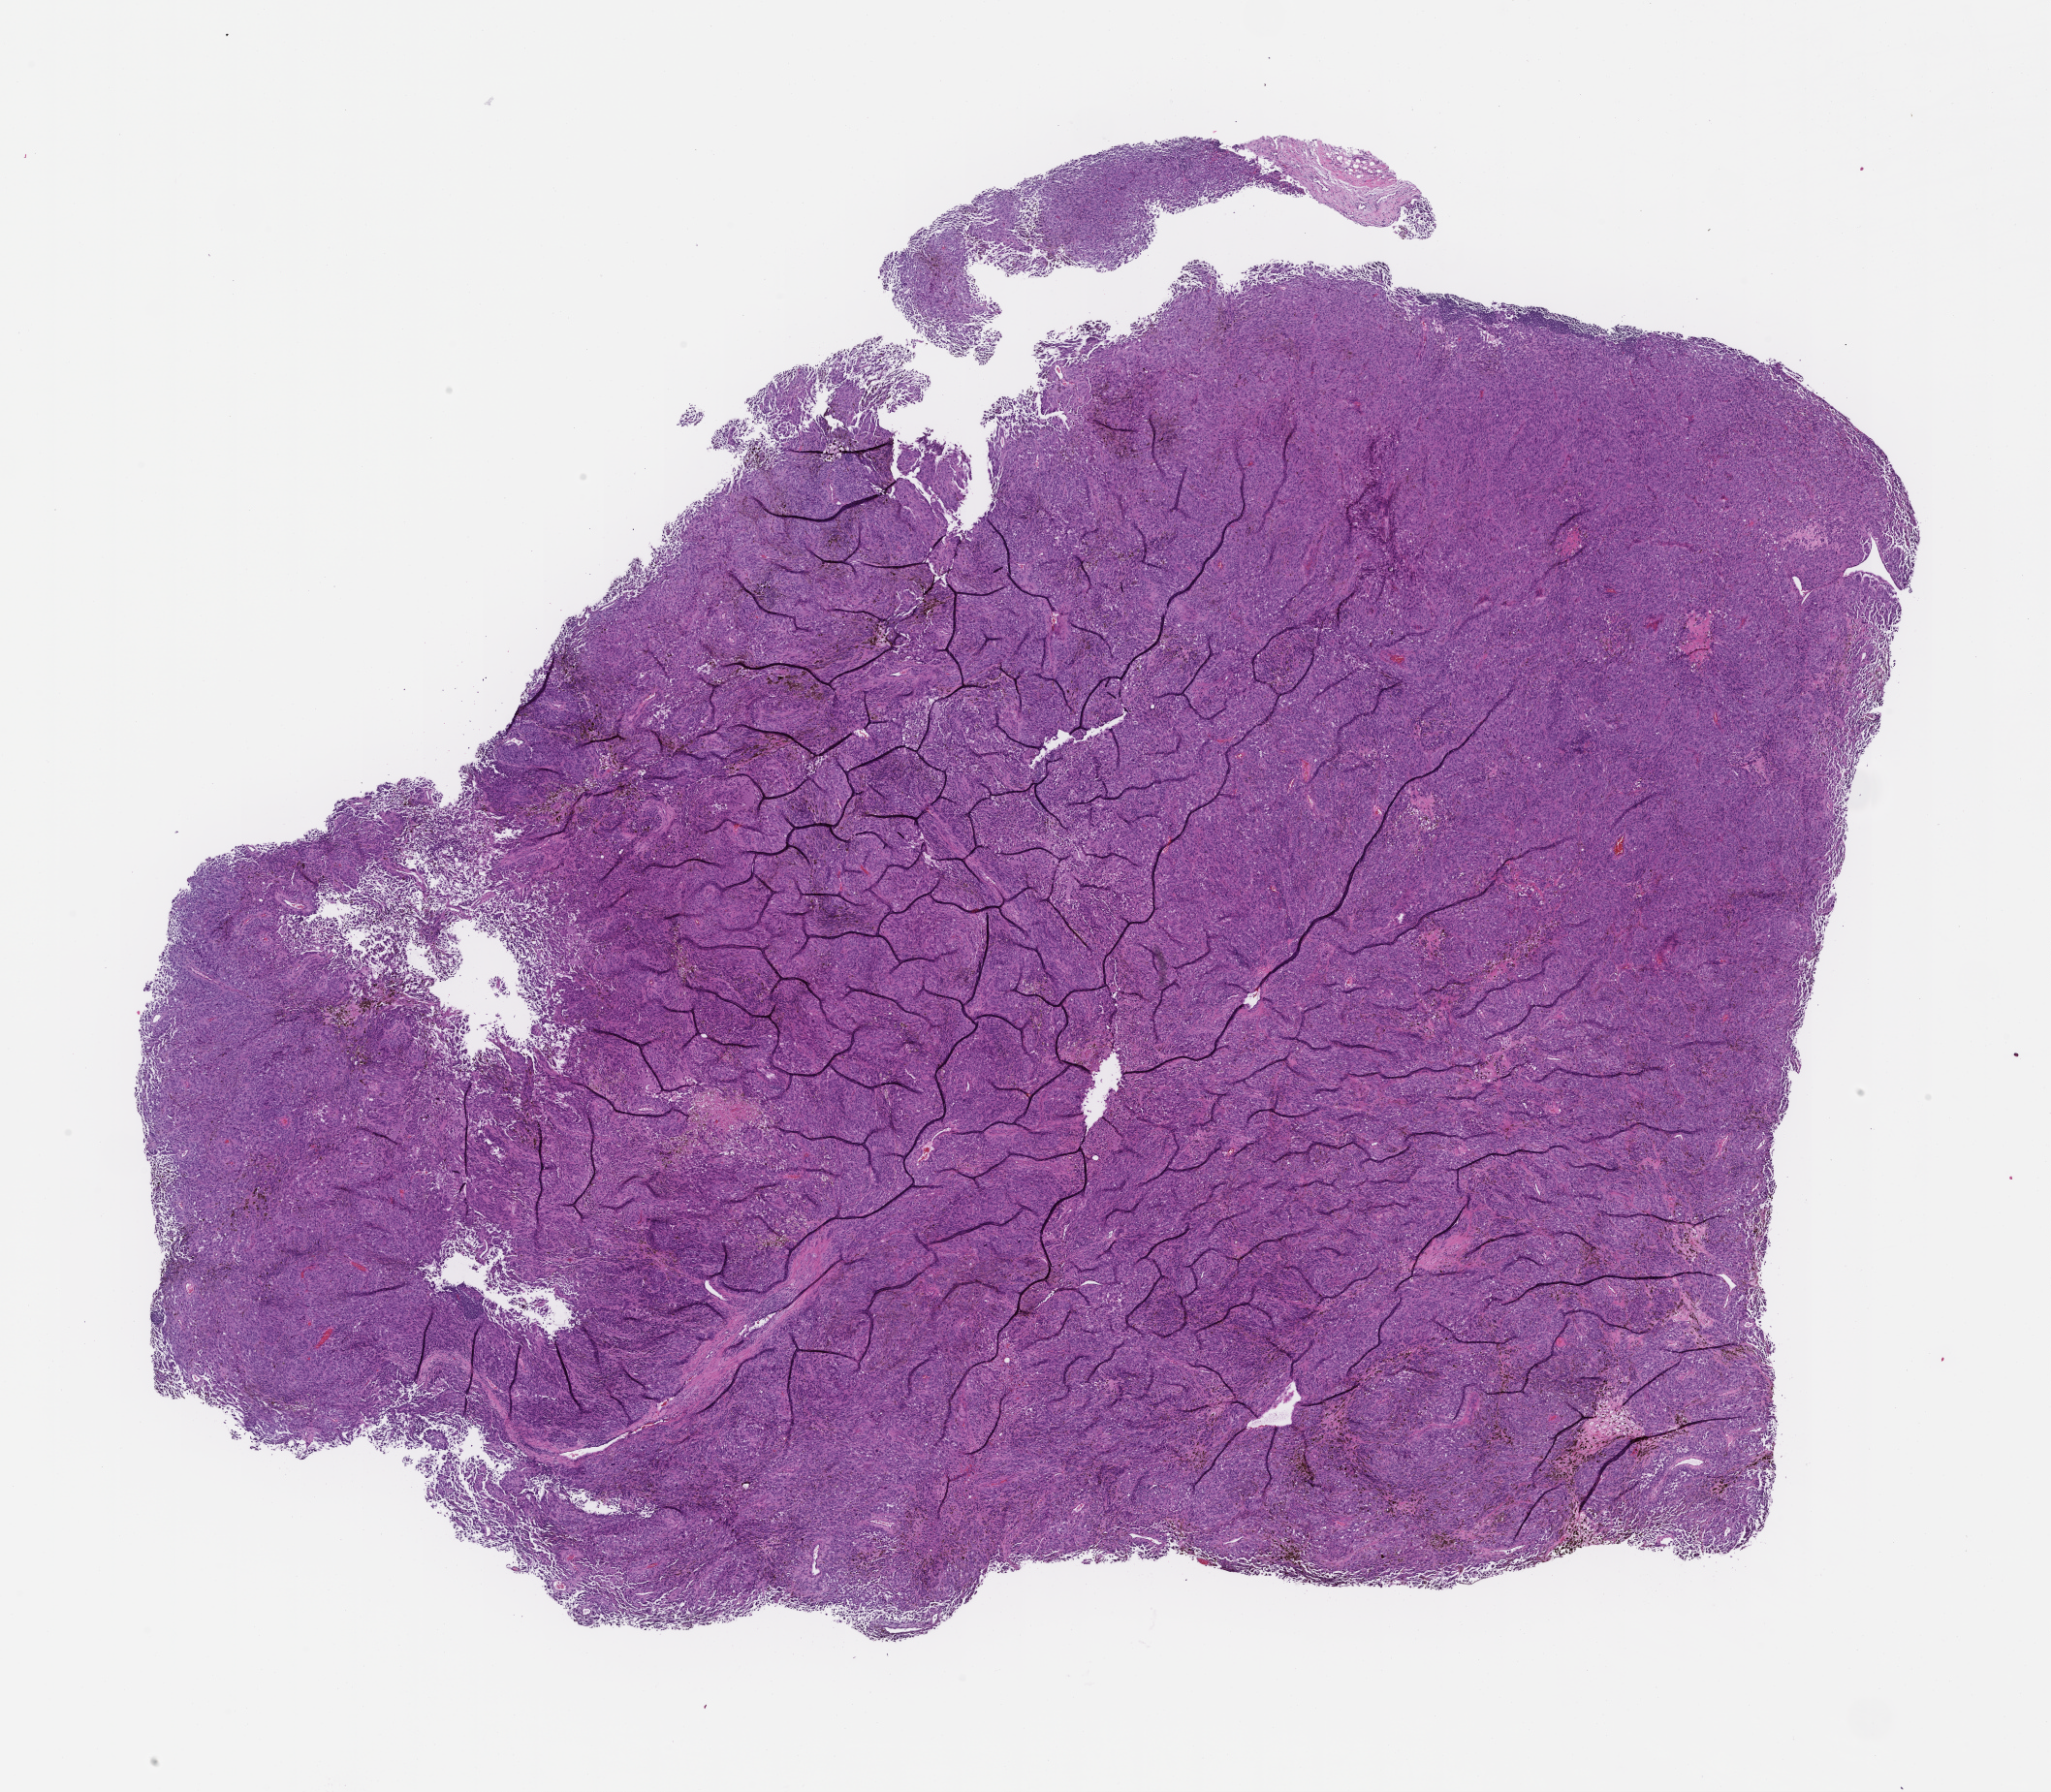
Digitized haematoxylin and eosin-stained section, shown as a low-resolution overview of the whole scanned area (about 17.1 x 14.9 mm); formalin-fixed, paraffin-embedded (FFPE) tissue. Patient sex: female.
This section: metastasis (sampled organ not recorded). Patient diagnosis (primary): Melanoma.